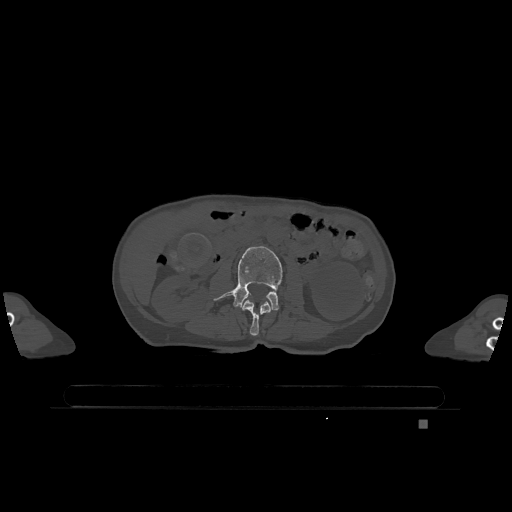
CT including the spine, one axial slice; slice 378 of 1317 in the series (ordered by position); bone window (W 1800 / L 400 HU); 0.5 mm slice thickness; 512 × 512 image matrix. Female patient, age 74 years. Case-level facts recorded for this patient, not image findings: primary cancer: lung.
Structures marked on this image (semi-automatically segmented with operator editing):
- L2 vertebra: bounding box (x1, y1, x2, y2) in pixels: (241, 299, 272, 336)
- L3 vertebra: (214, 246, 283, 311)